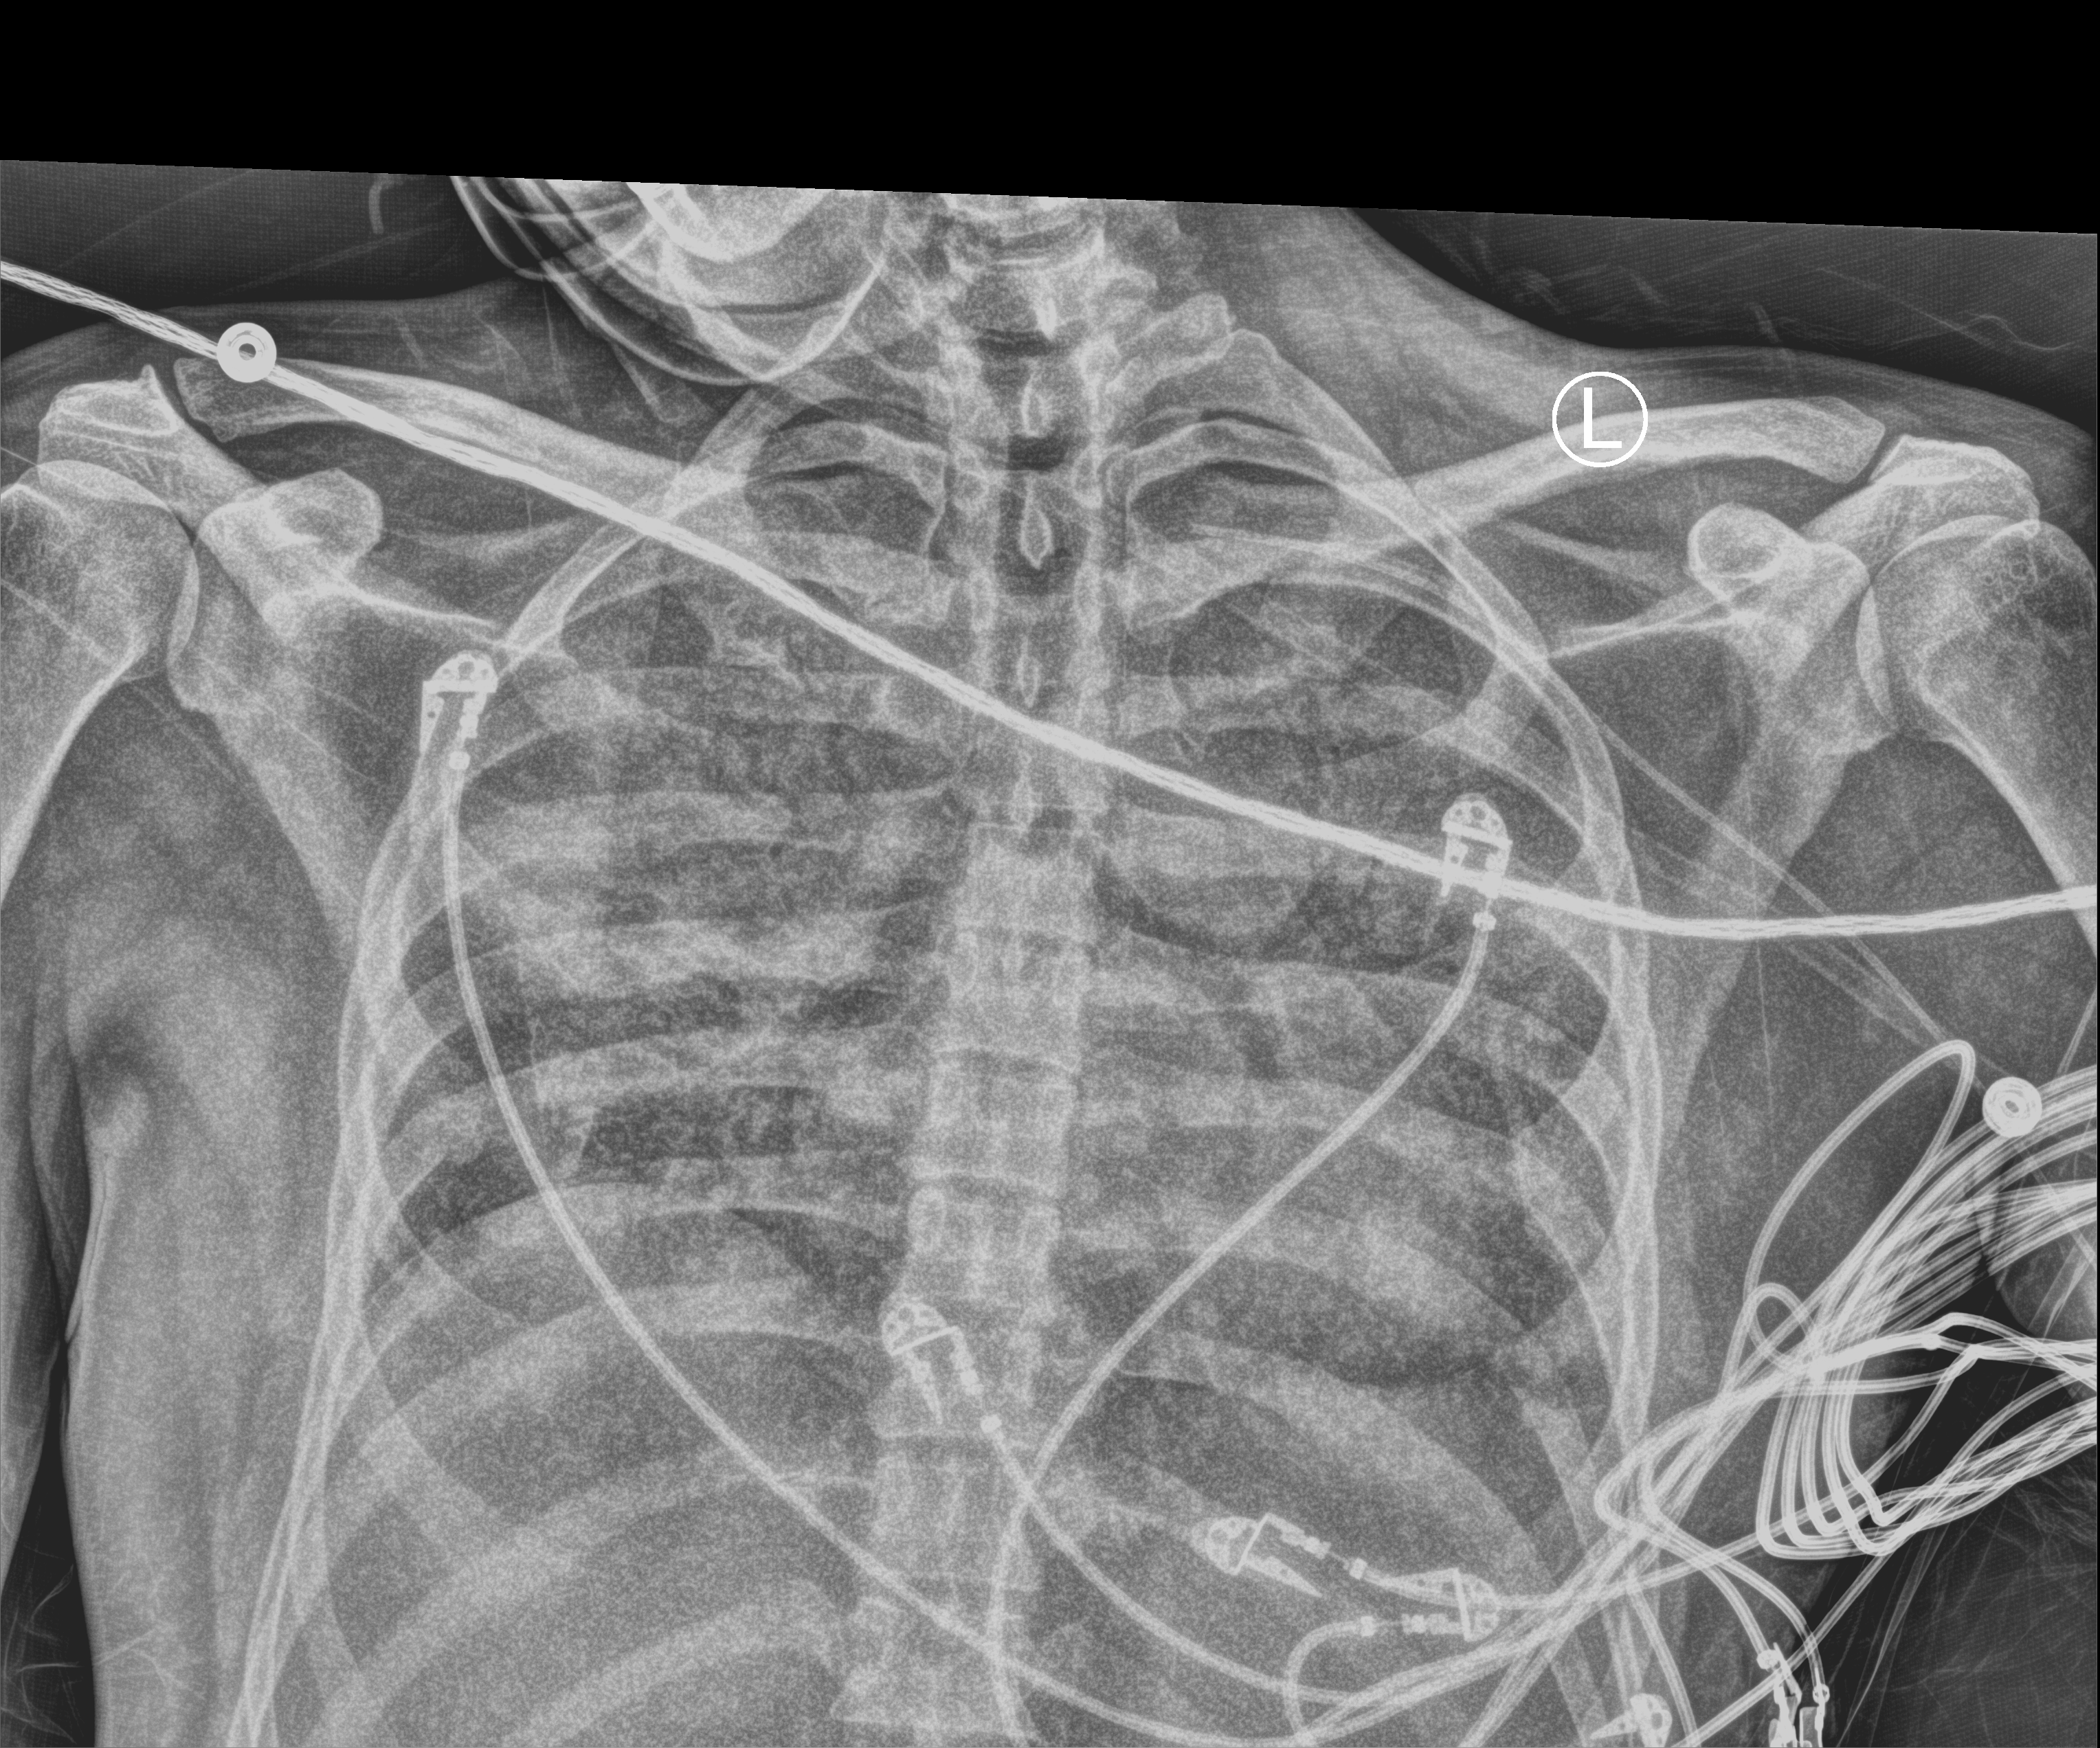
Bedside chest radiograph (computed radiography). Patient hospitalised with COVID-19; male, aged 18–59 years.
Hospital-stay facts (about this admission, not read from this image; timing relative to this image not recorded):
- admitted to intensive care during this hospital stay: yes